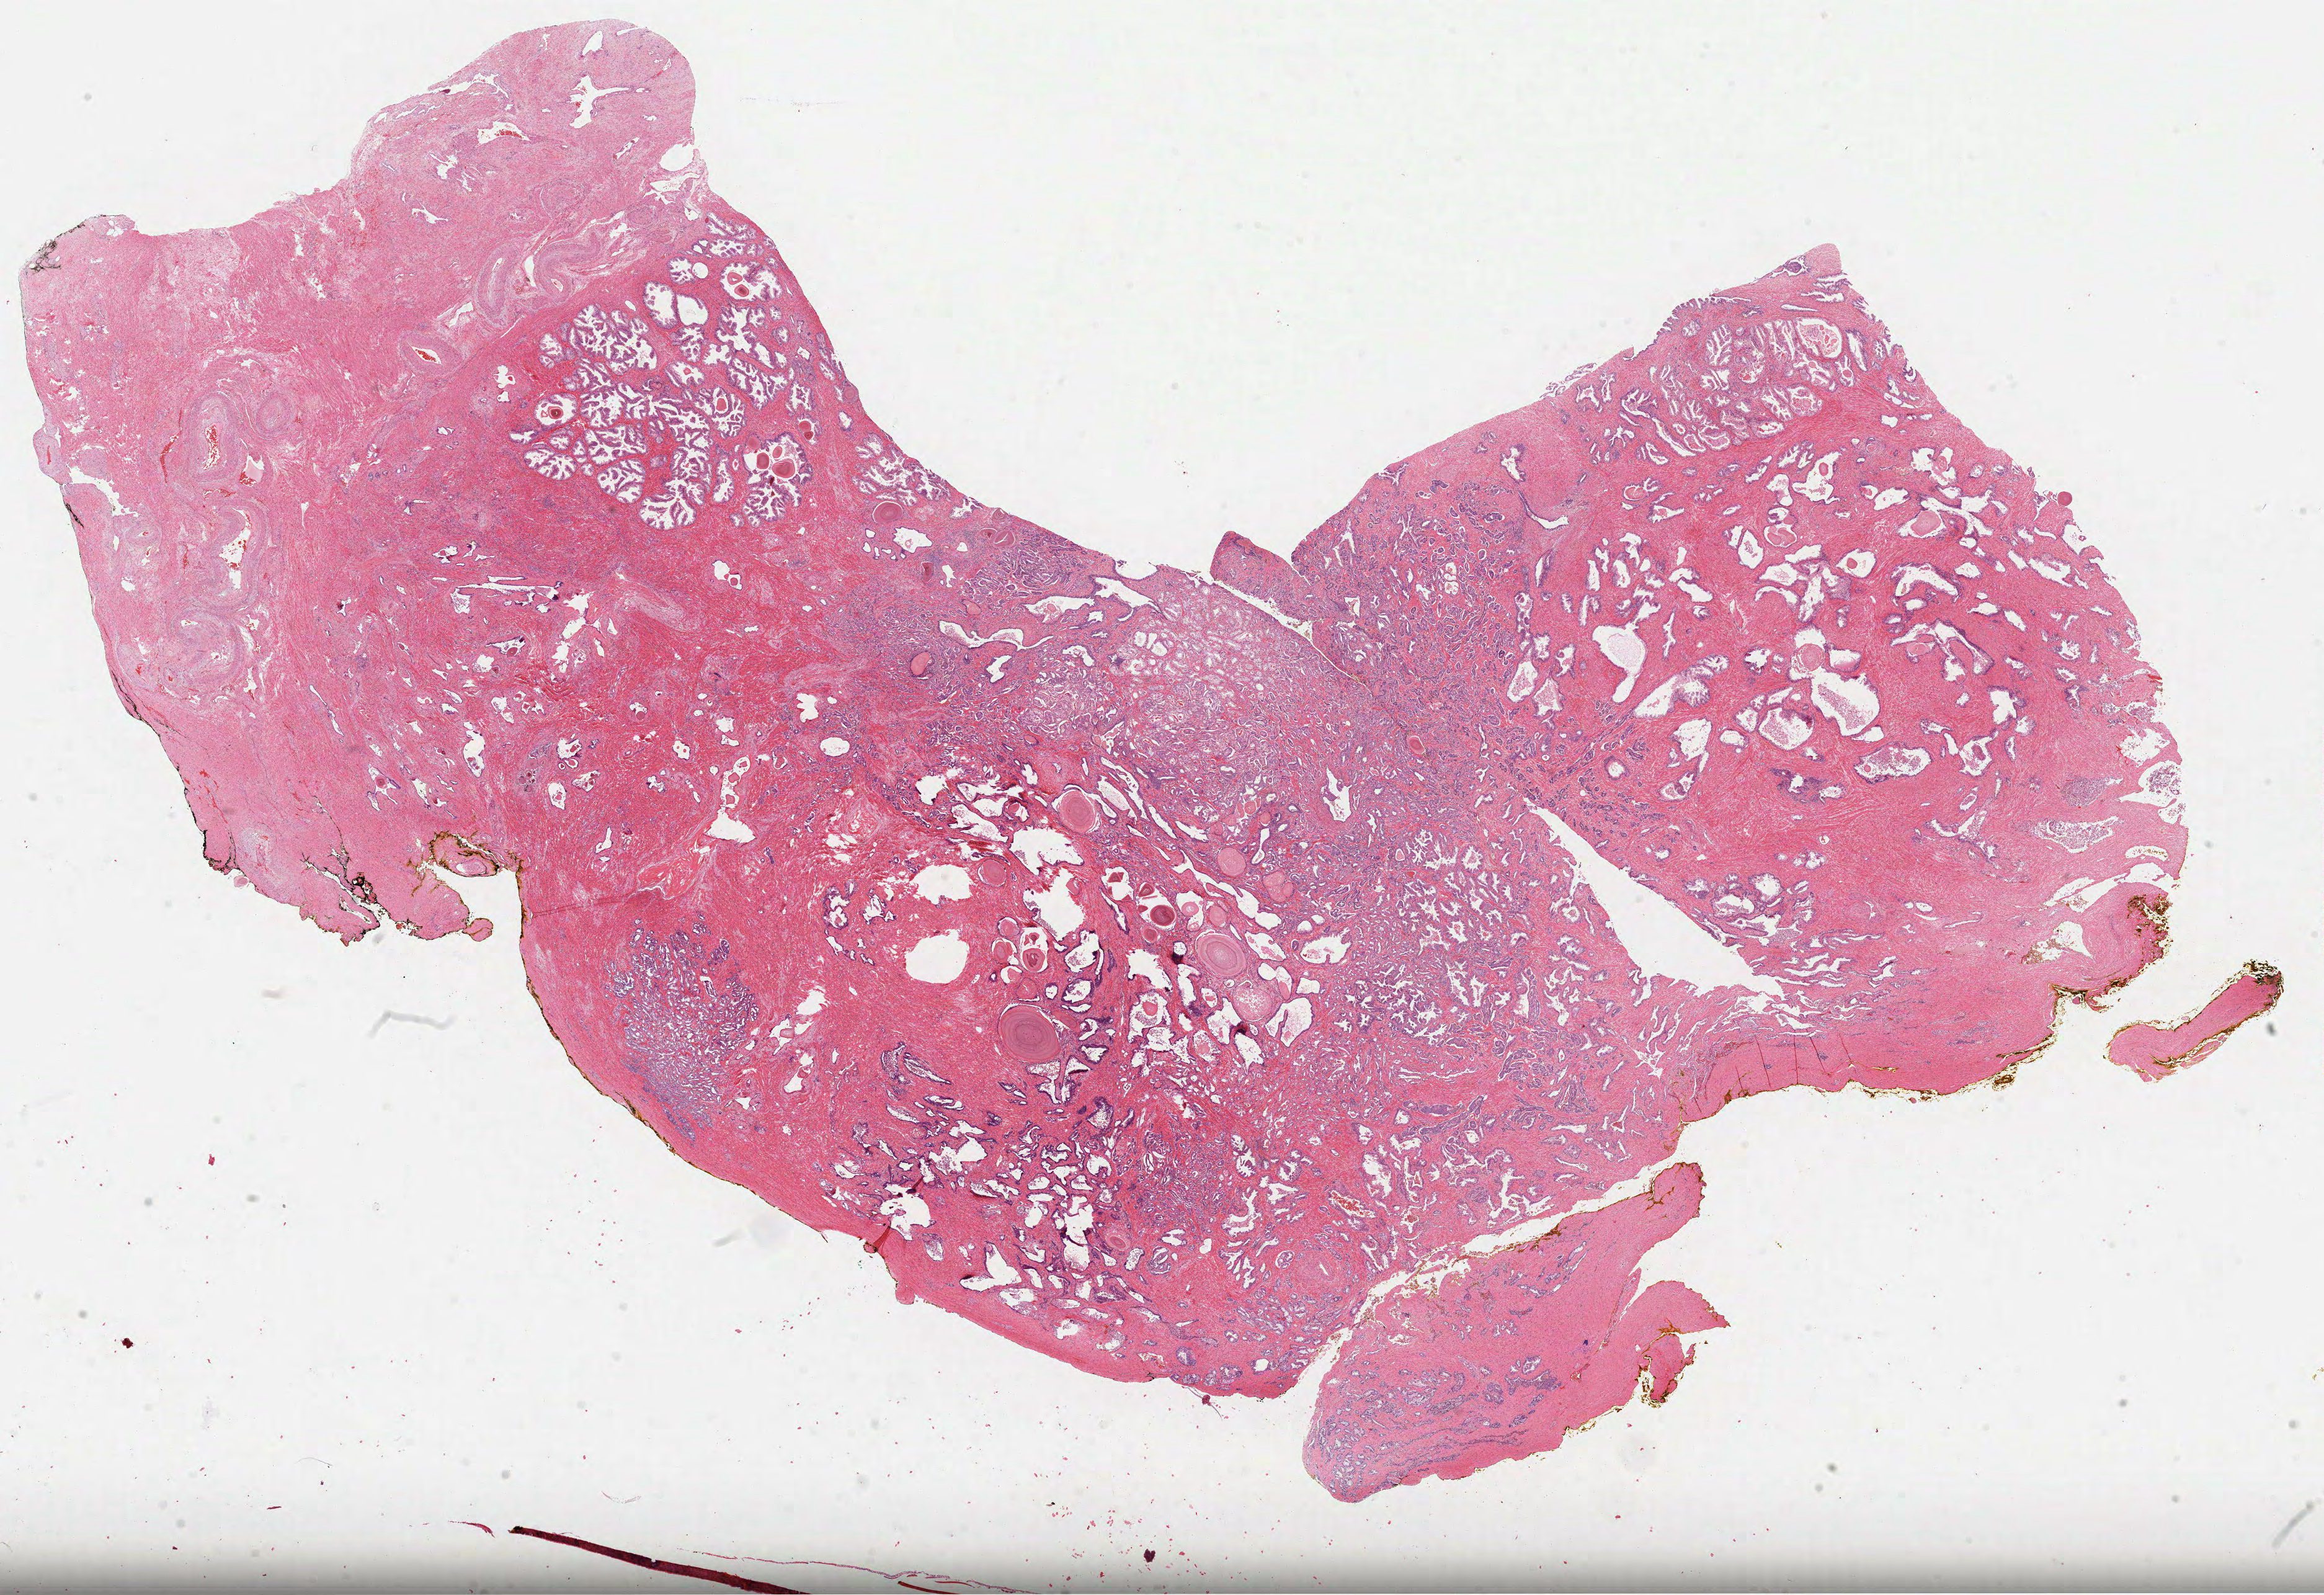
Digitized Hematoxylin and eosin (H&E) stained tissue section (whole slide) — shown as a low-resolution overview of the whole scanned area (about 30.2 x 20.7 mm, slide scanned at 40x); formalin-fixed paraffin-embedded (FFPE) diagnostic section; primary tumour sample from the prostate. Male patient; age at initial diagnosis 67 years. Gleason score: 7 (3+4).
Pathologic diagnosis: Acinar cell carcinoma (prostate gland).